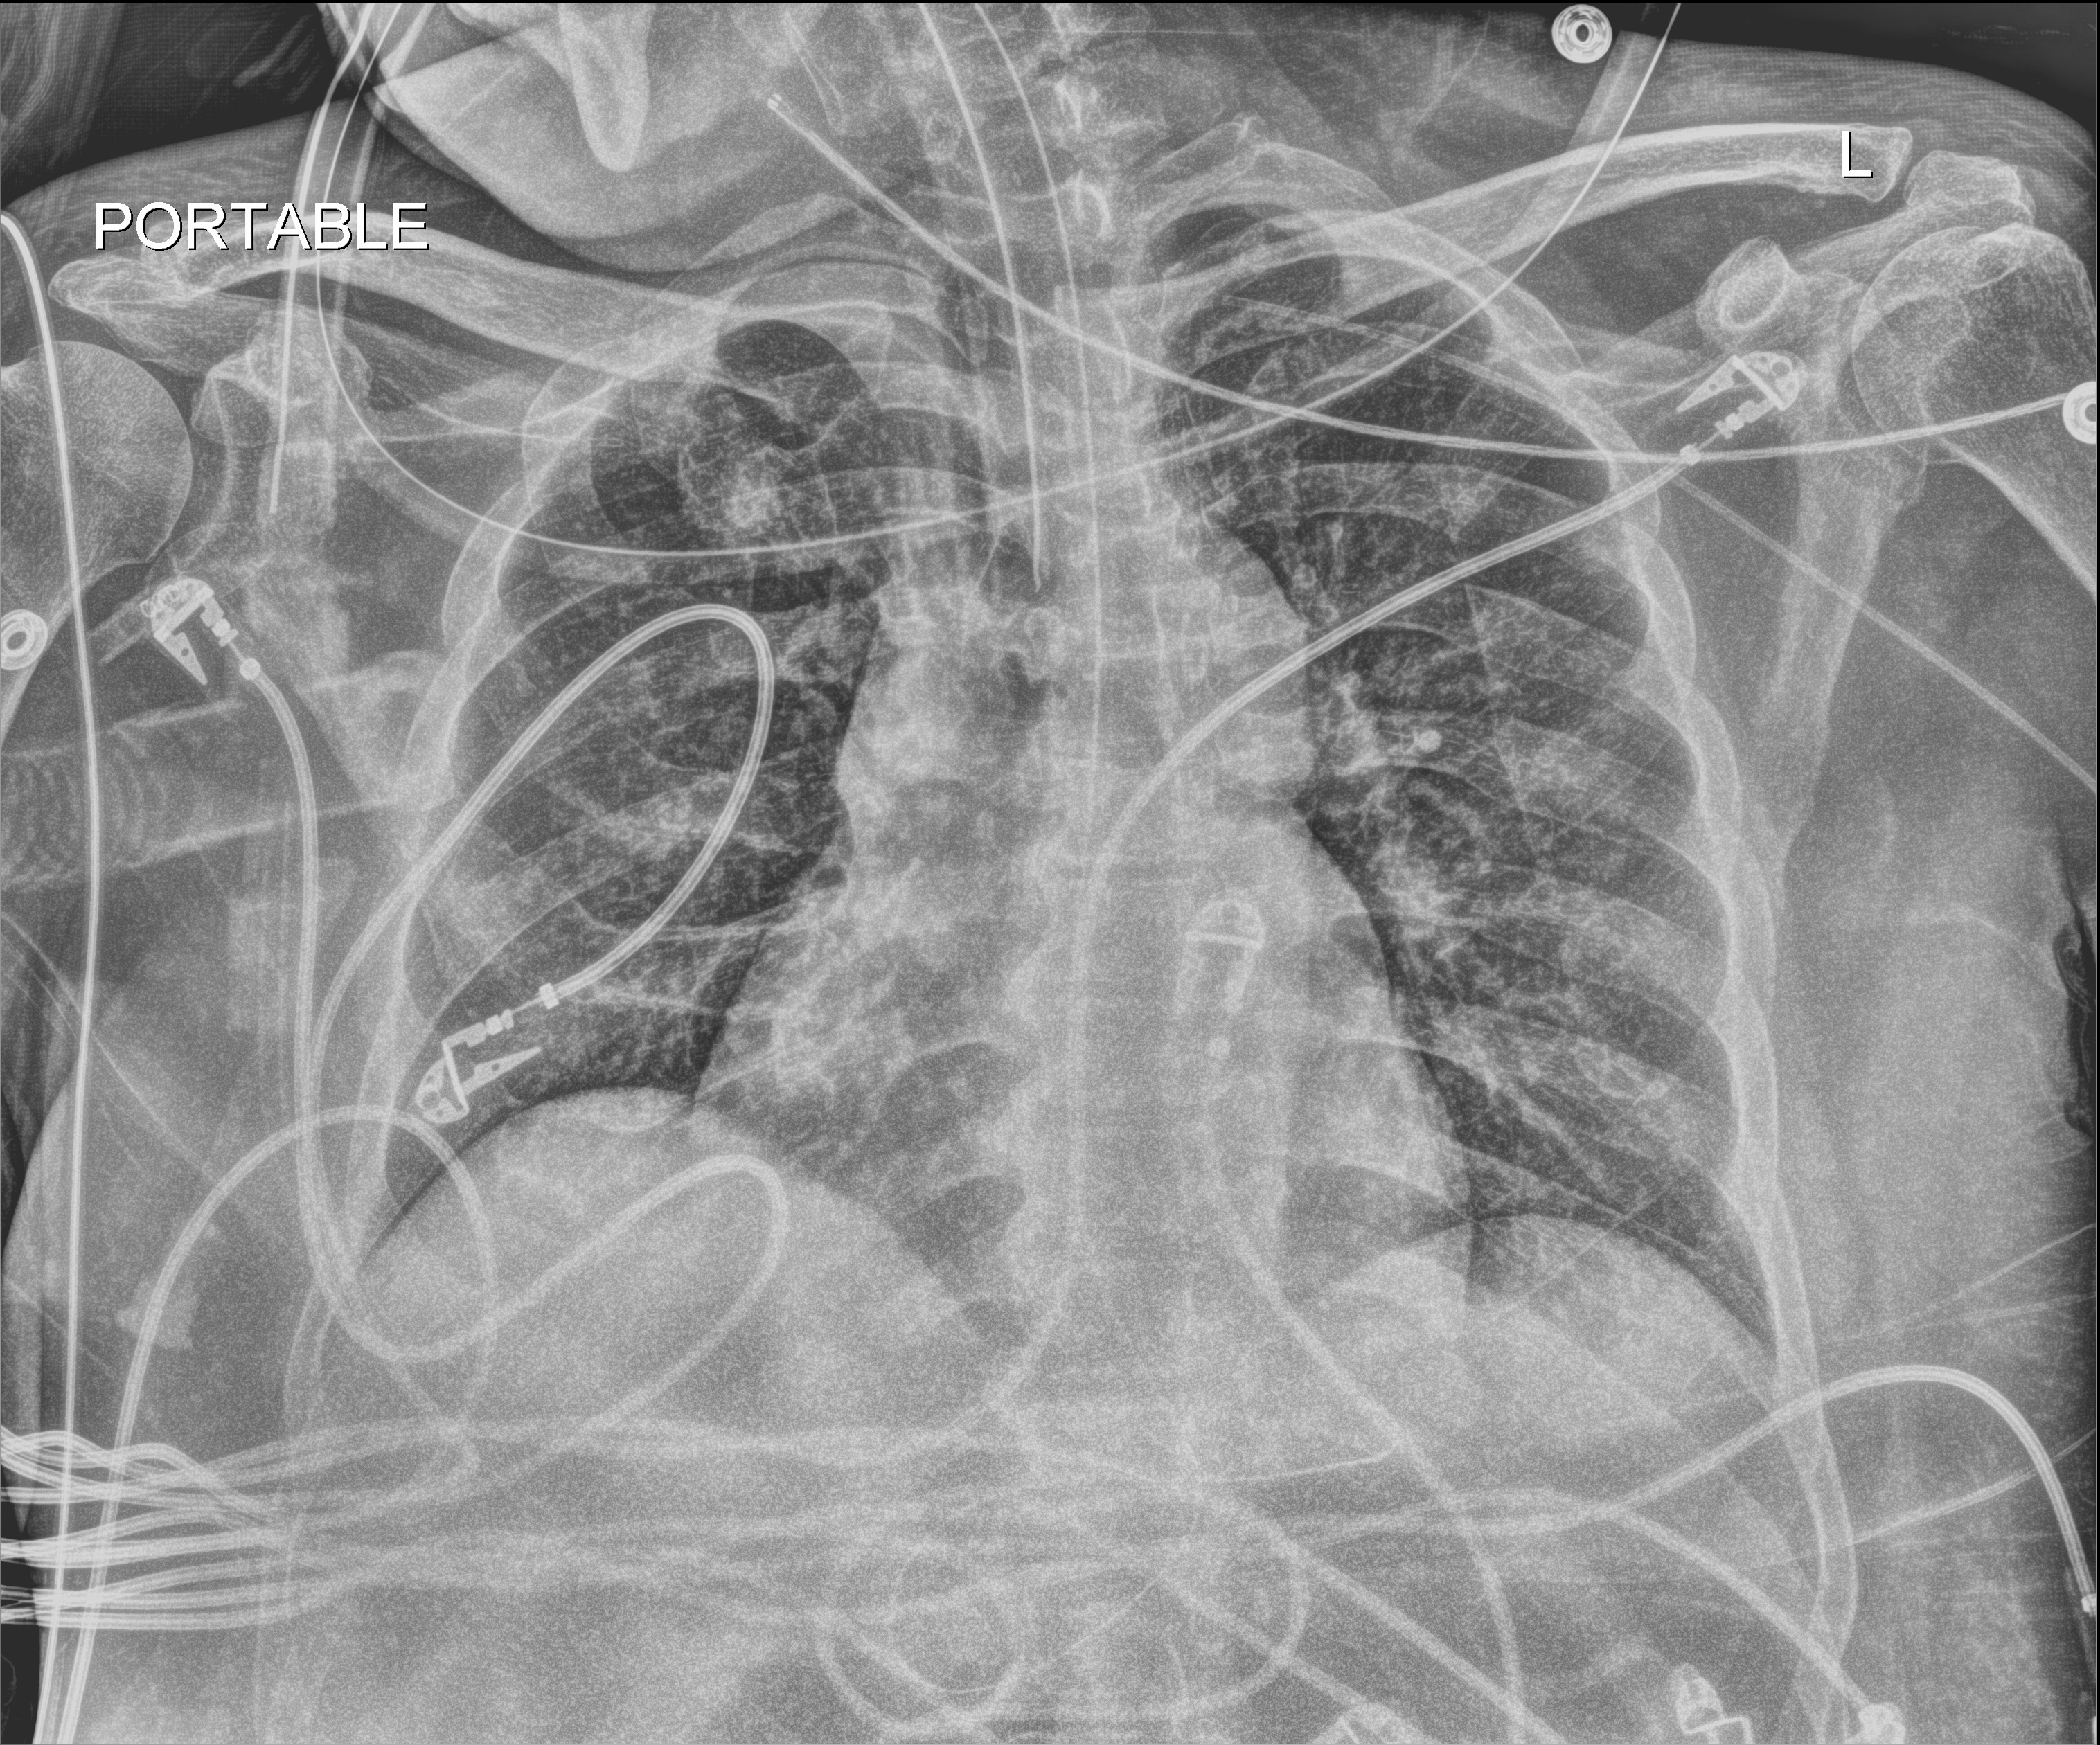
Bedside chest radiograph (digital radiography), anteroposterior (AP) projection. Patient hospitalised with COVID-19, aged 18–59 years.
From the hospital-stay record, not from the radiograph (when in the stay this image was taken is not recorded): length of hospital stay: 37 days; hypertension (admission record): no.